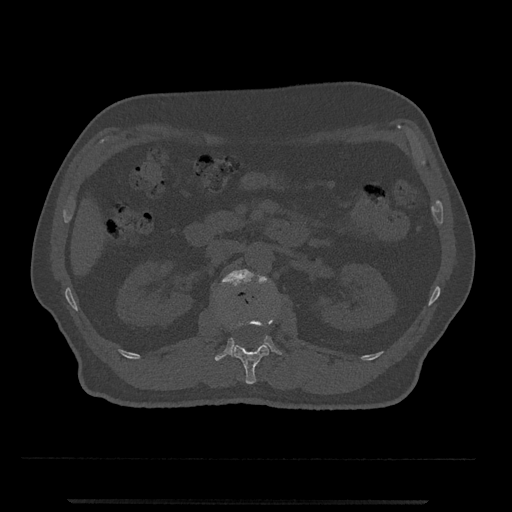
CT including the spine, one axial slice. Position 305 of 797 along the scan axis. Bone window (W 1800 / L 400 HU). 0.5 mm slice thickness. 512 × 512 image matrix, field of view 419 × 419 mm. Patient: male, 63 years. Case-level facts recorded for this patient, not image findings: primary cancer: prostate.
Annotated regions visible in this slice (semi-automatically segmented with operator editing):
- L1 vertebra: bounding box [x1, y1, x2, y2] px = [229, 317, 274, 384]
- L2 vertebra: [215, 269, 282, 361]